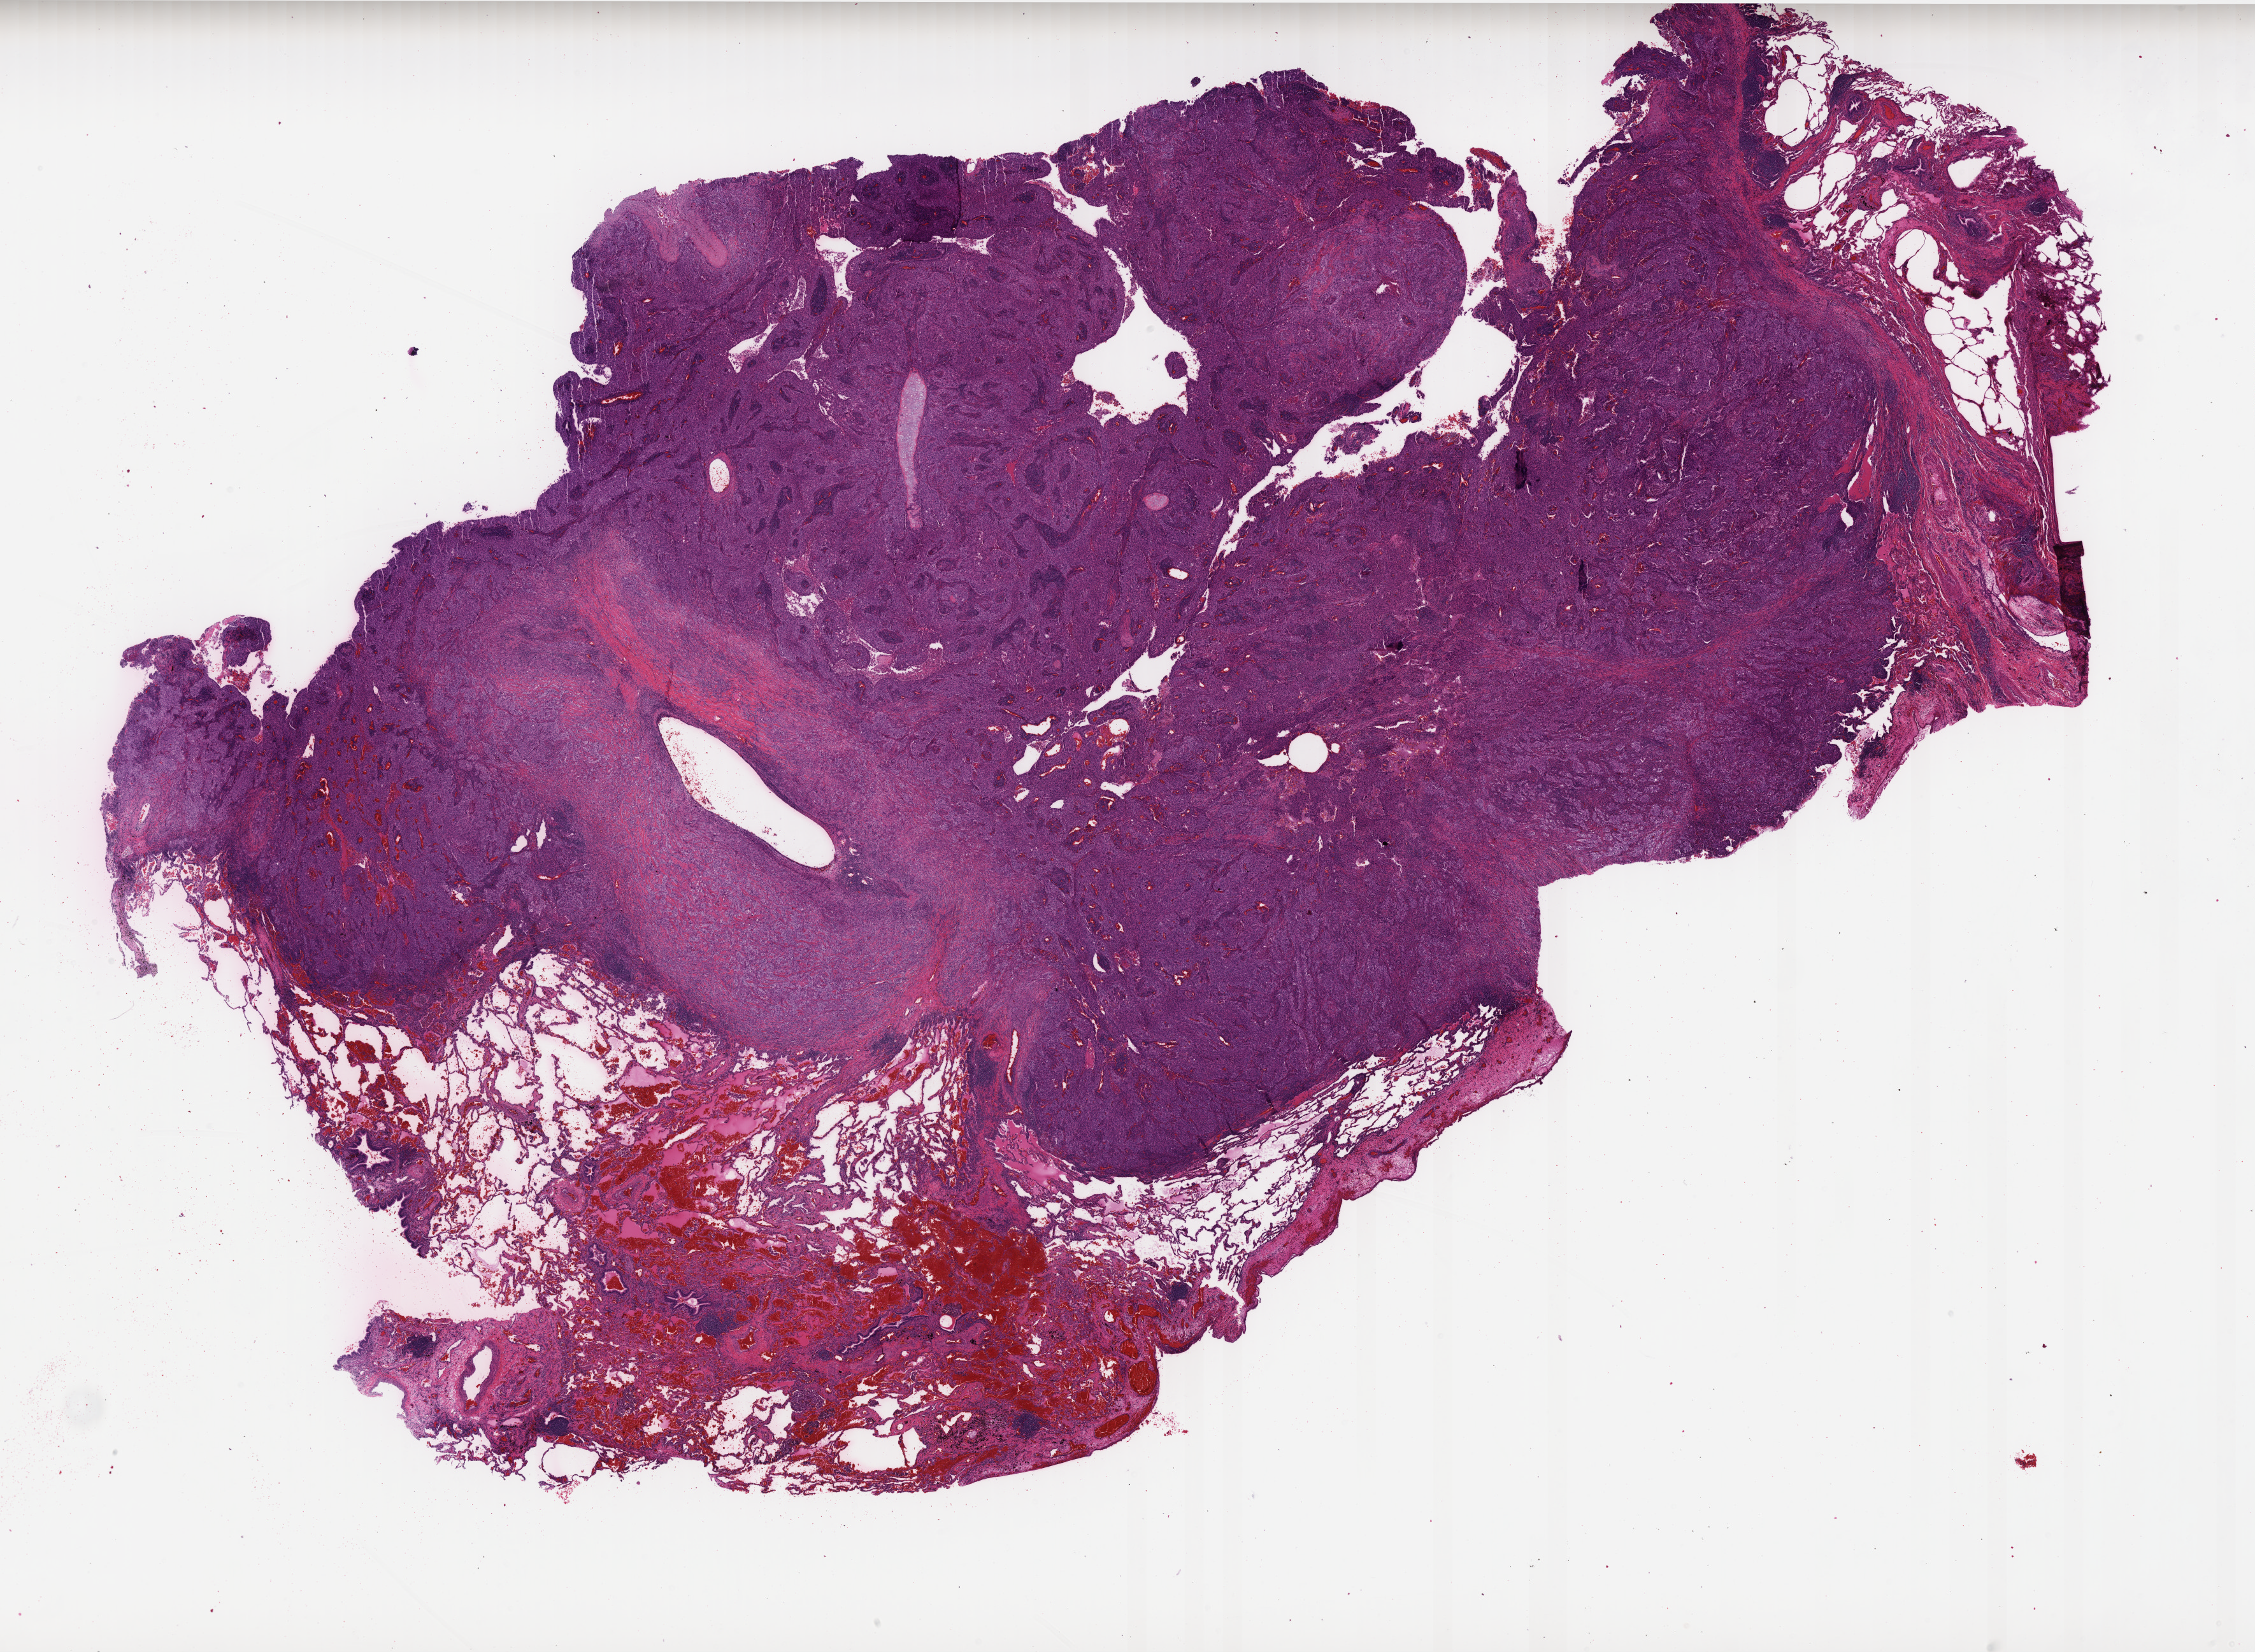
Whole-slide histology image, Hematoxylin and eosin (H&E) stained — low-resolution overview of the scanned area, about 28.4 x 20.8 mm (slide scanned at 40x); formalin-fixed paraffin-embedded (FFPE) diagnostic section; lung, primary tumour sample. Female patient; age at initial diagnosis 46 years.
* laterality: right
* diagnosis: Adenocarcinoma, NOS
* AJCC pathologic stage: IIB (7th edition)